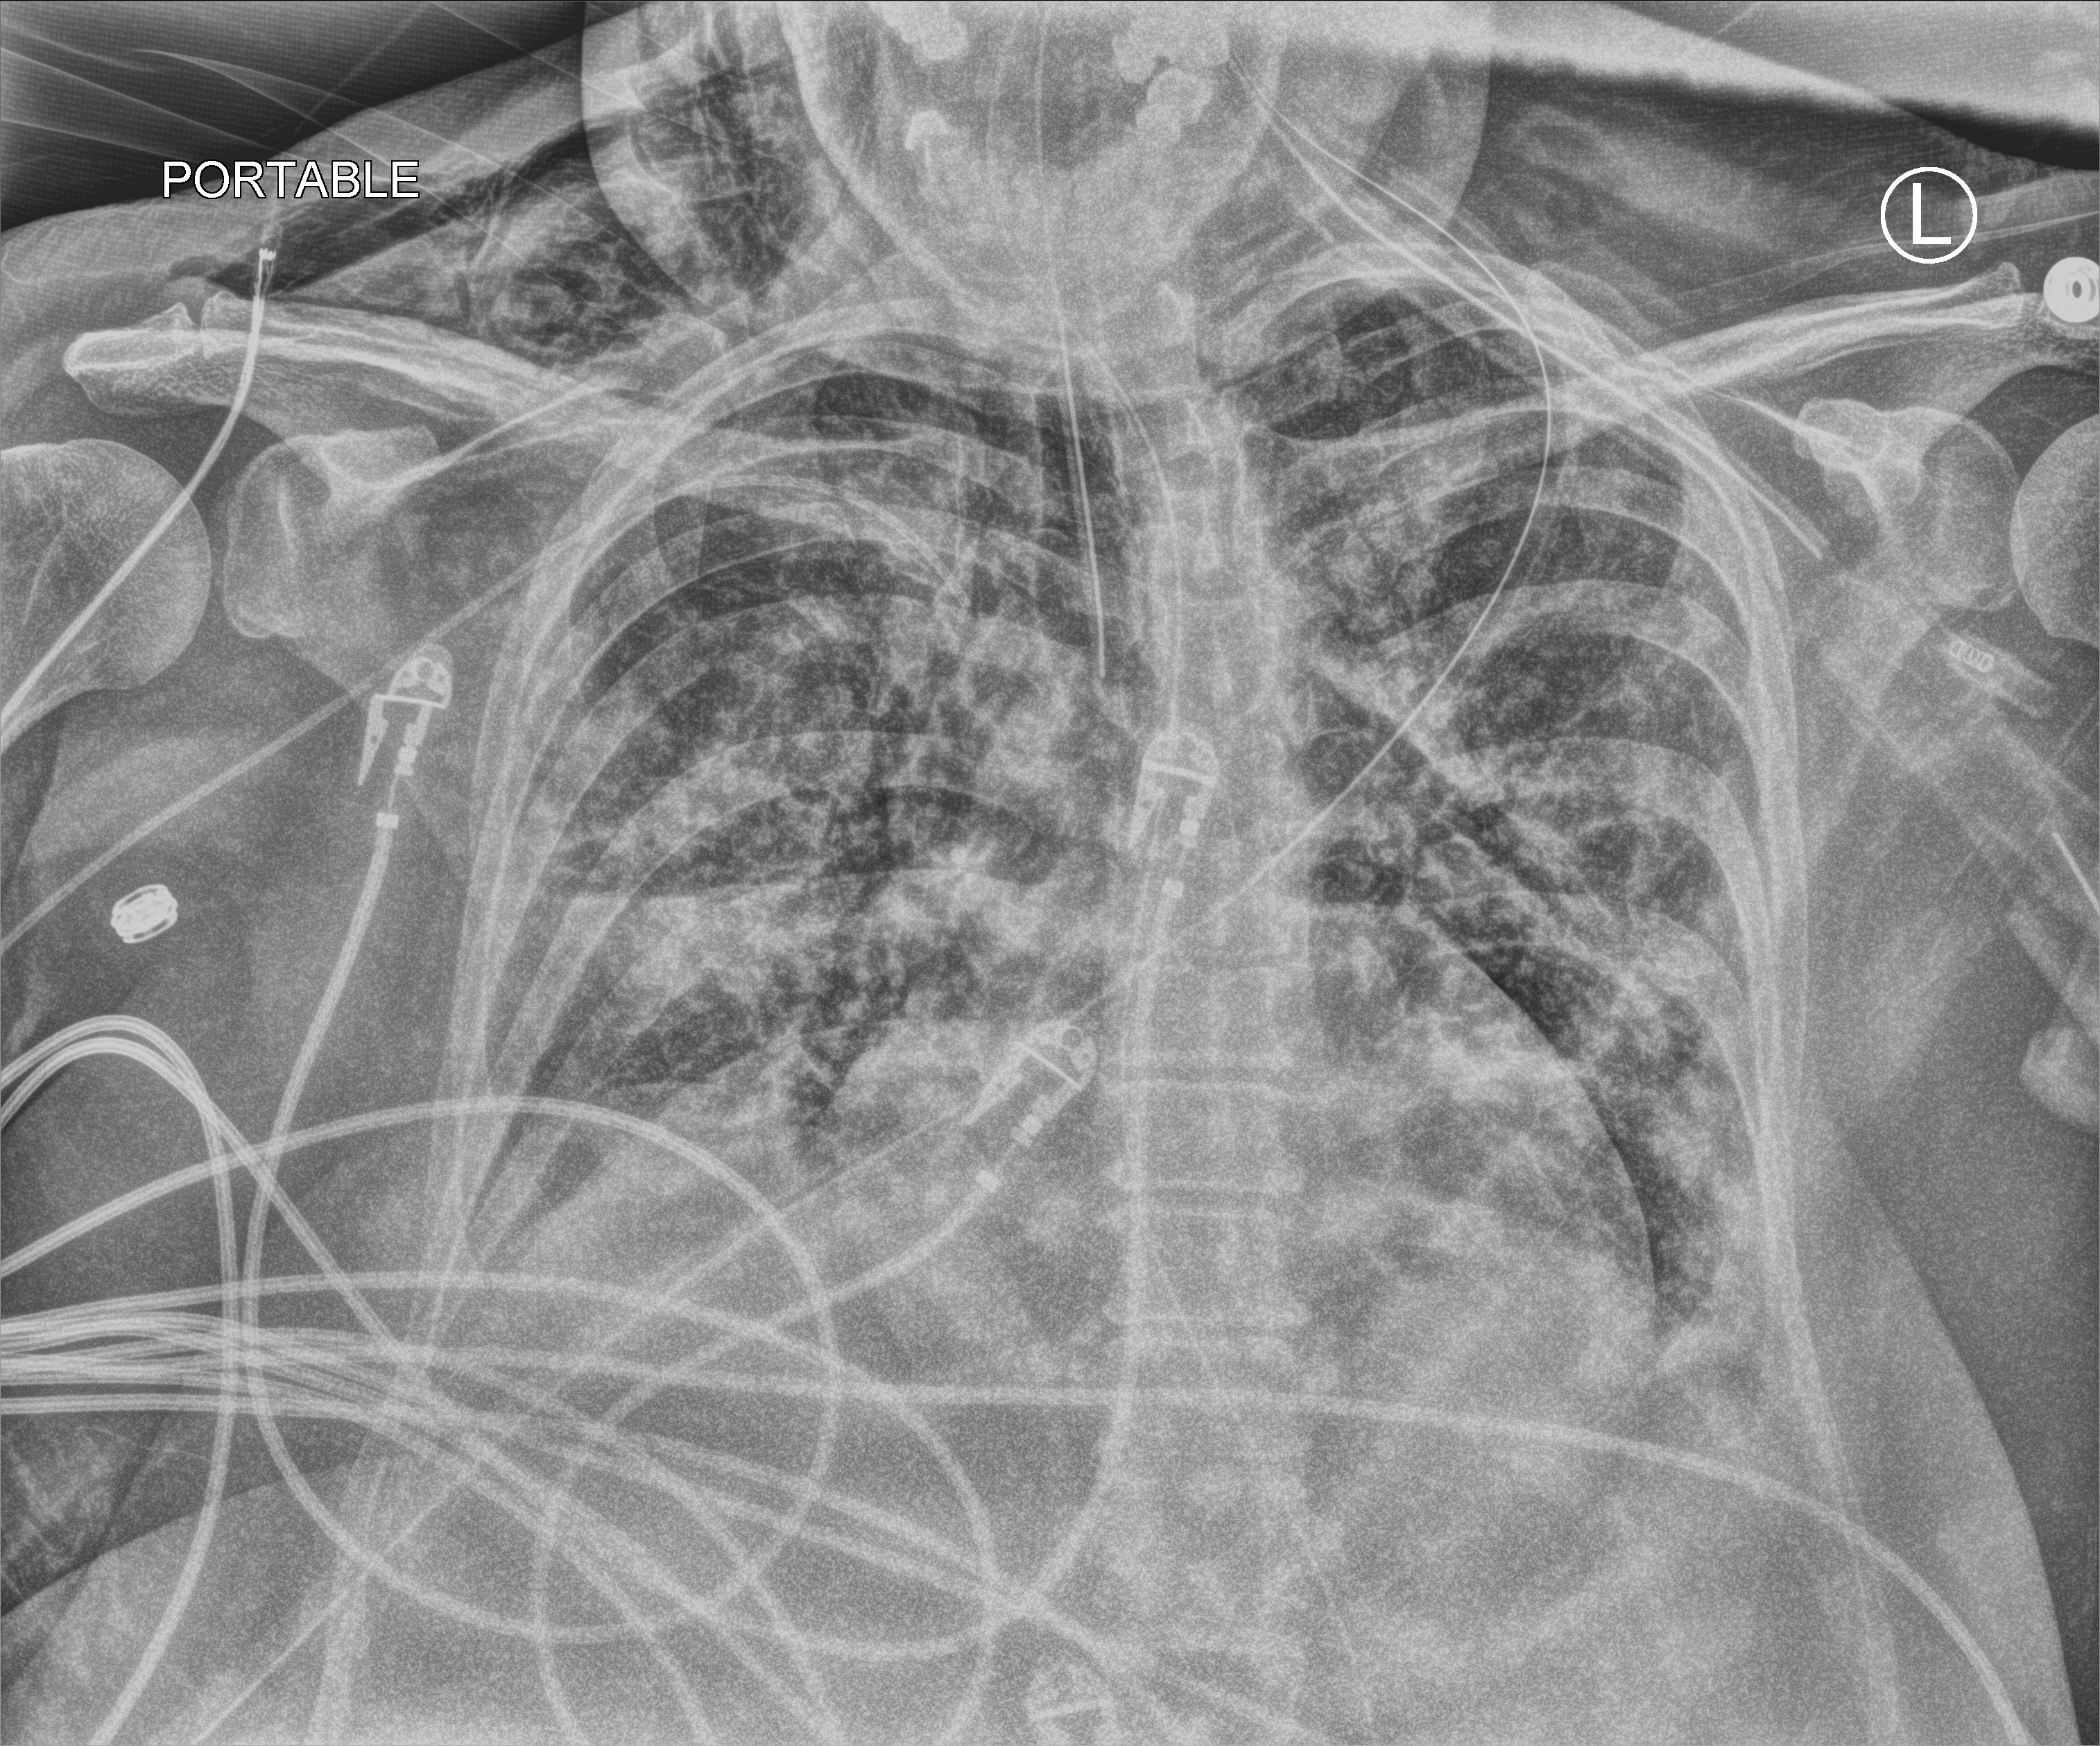
Bedside chest radiograph (computed radiography). Patient hospitalised with COVID-19; female, aged 60–74 years.
Admission-level facts for this patient (not findings on this image; timing relative to this image not recorded): mechanically ventilated during this hospital stay: yes; other chronic lung disease (admission record): yes.